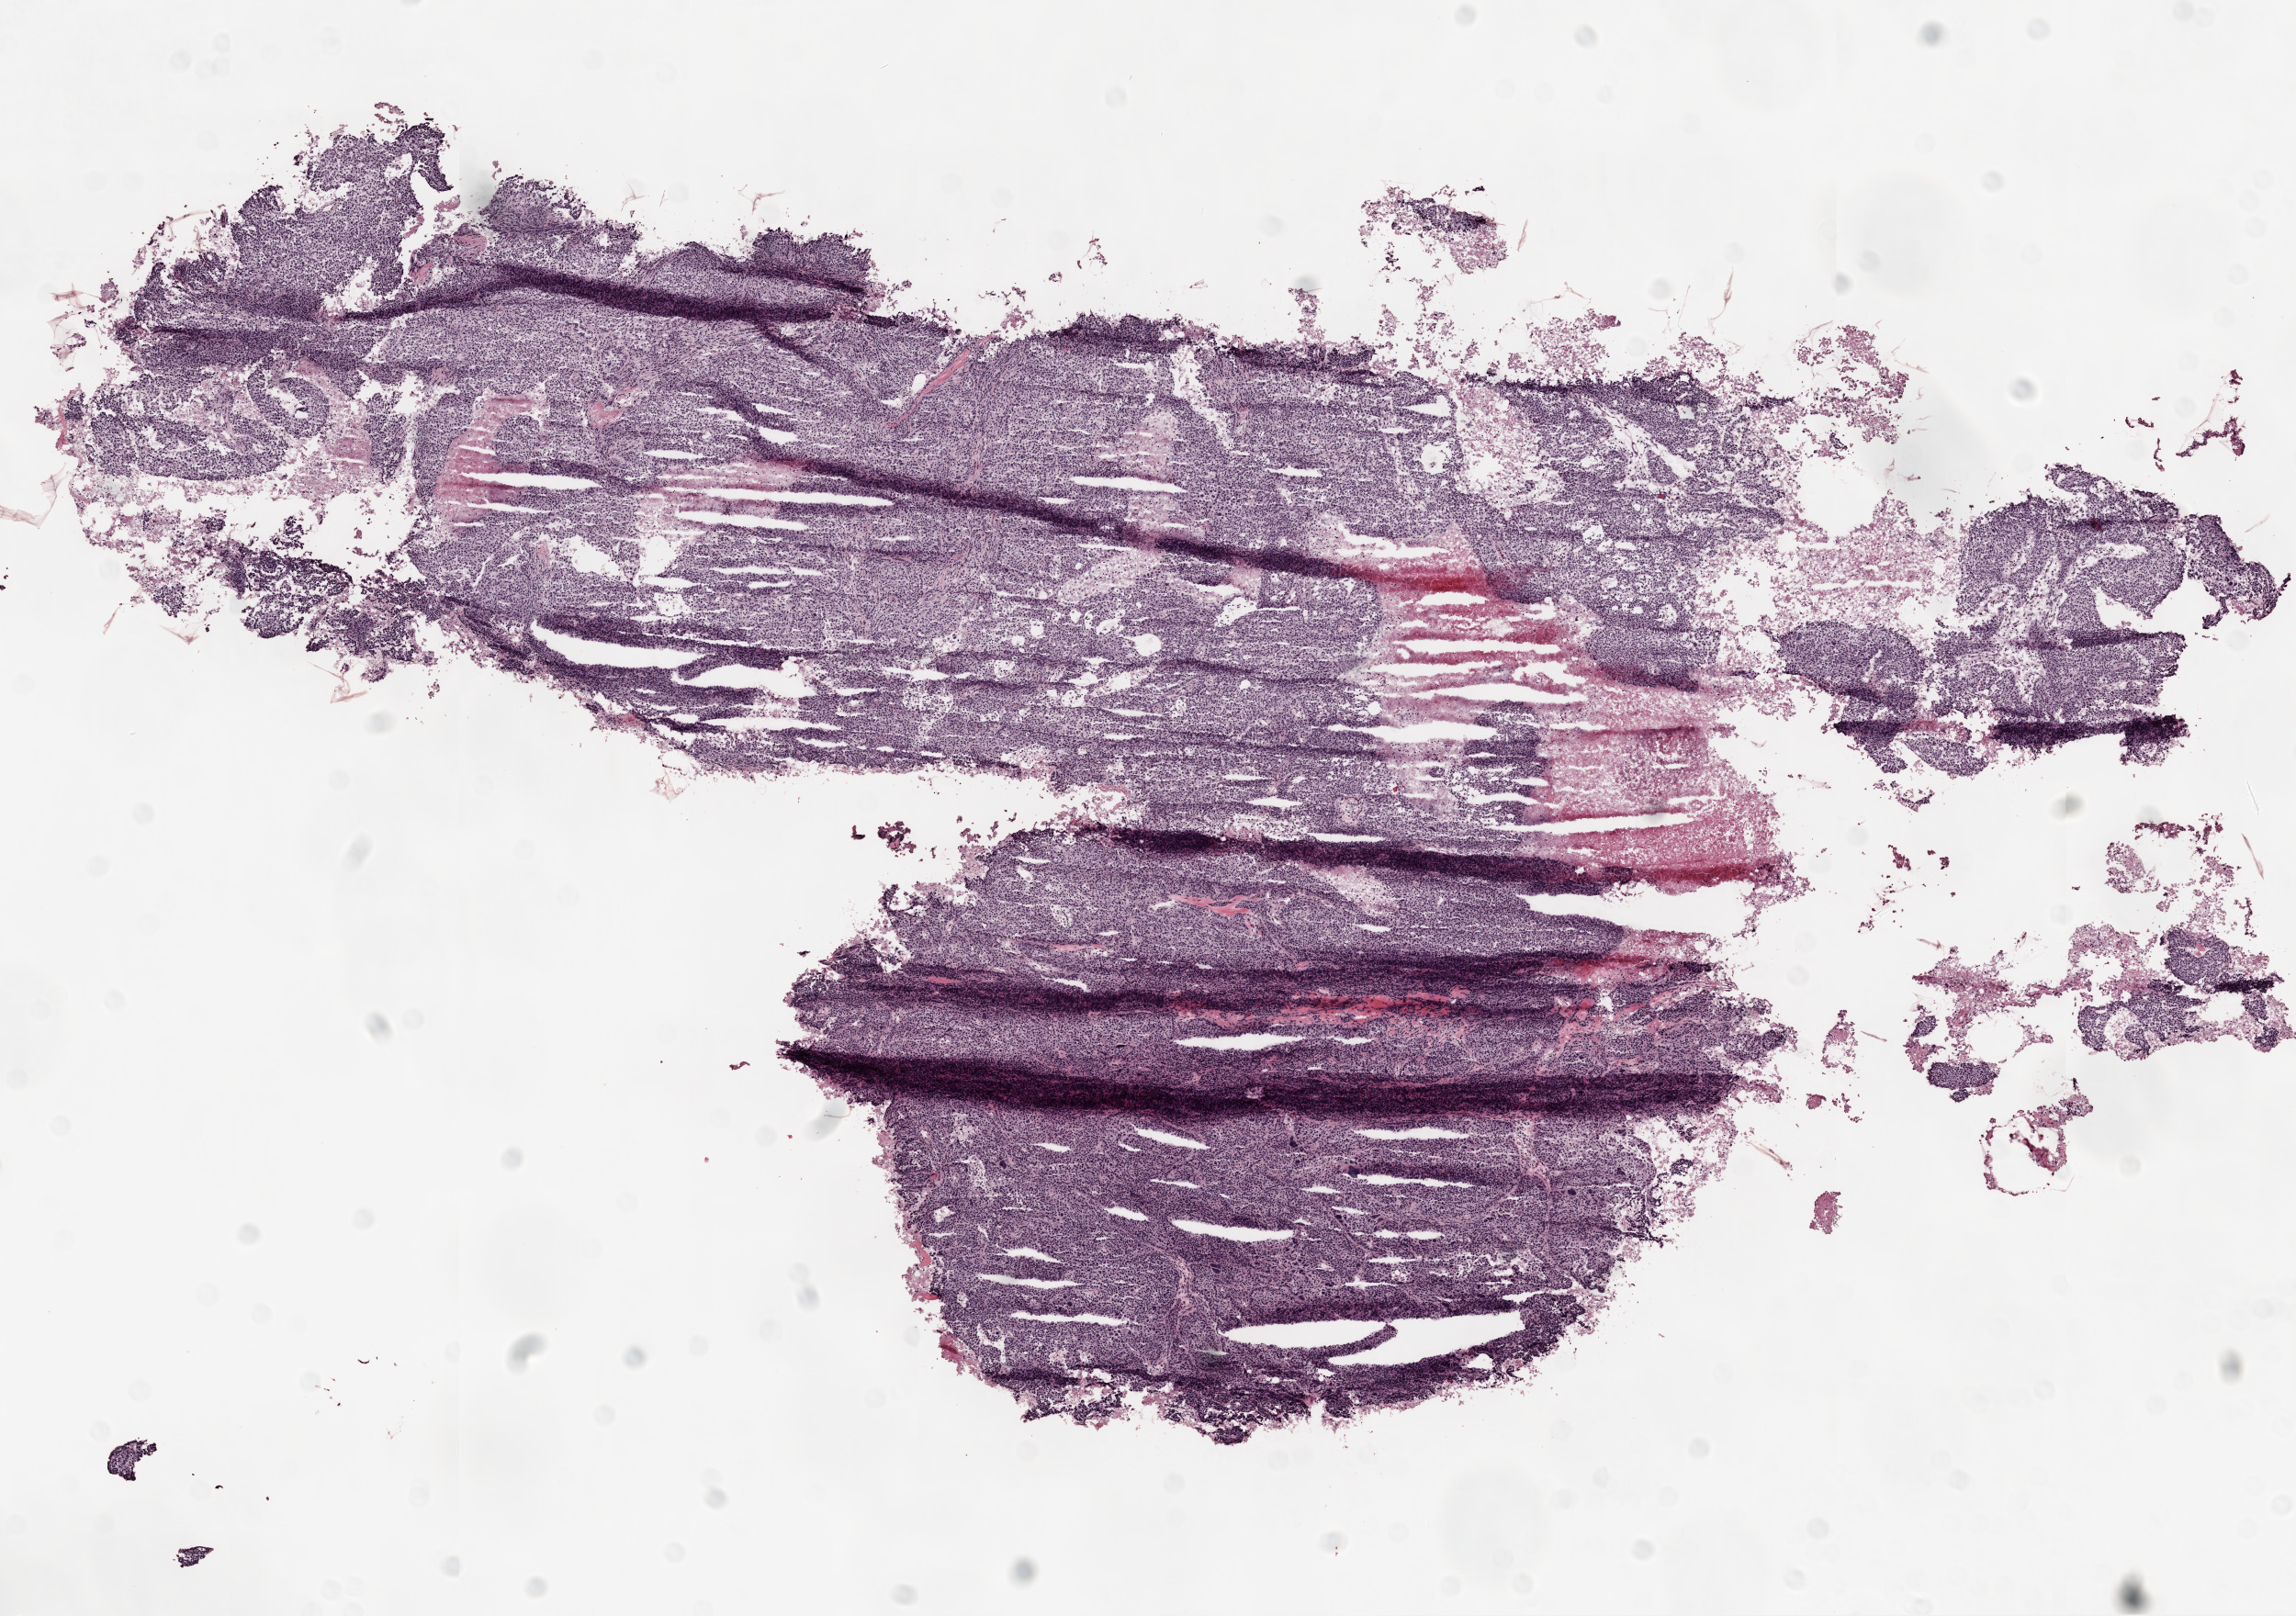
Whole-slide histology image, H&E — a low-resolution overview of the entire scanned area, about 10.0 x 7.1 mm (from a 20x scan); frozen section from the top of the tissue portion; primary tumour sample from the ovary. Female, age 69 years at initial diagnosis. Histologic grade: G3 (poorly differentiated). Slide review estimates, as recorded: tumour cells 80%, tumour nuclei 90%, normal cells 0%, stromal cells 0%, necrosis 20%. Infiltration values recorded for this section: lymphocyte infiltration 5%.
Histologic diagnosis: Serous cystadenocarcinoma, NOS. FIGO stage: IIIC. Laterality: bilateral.